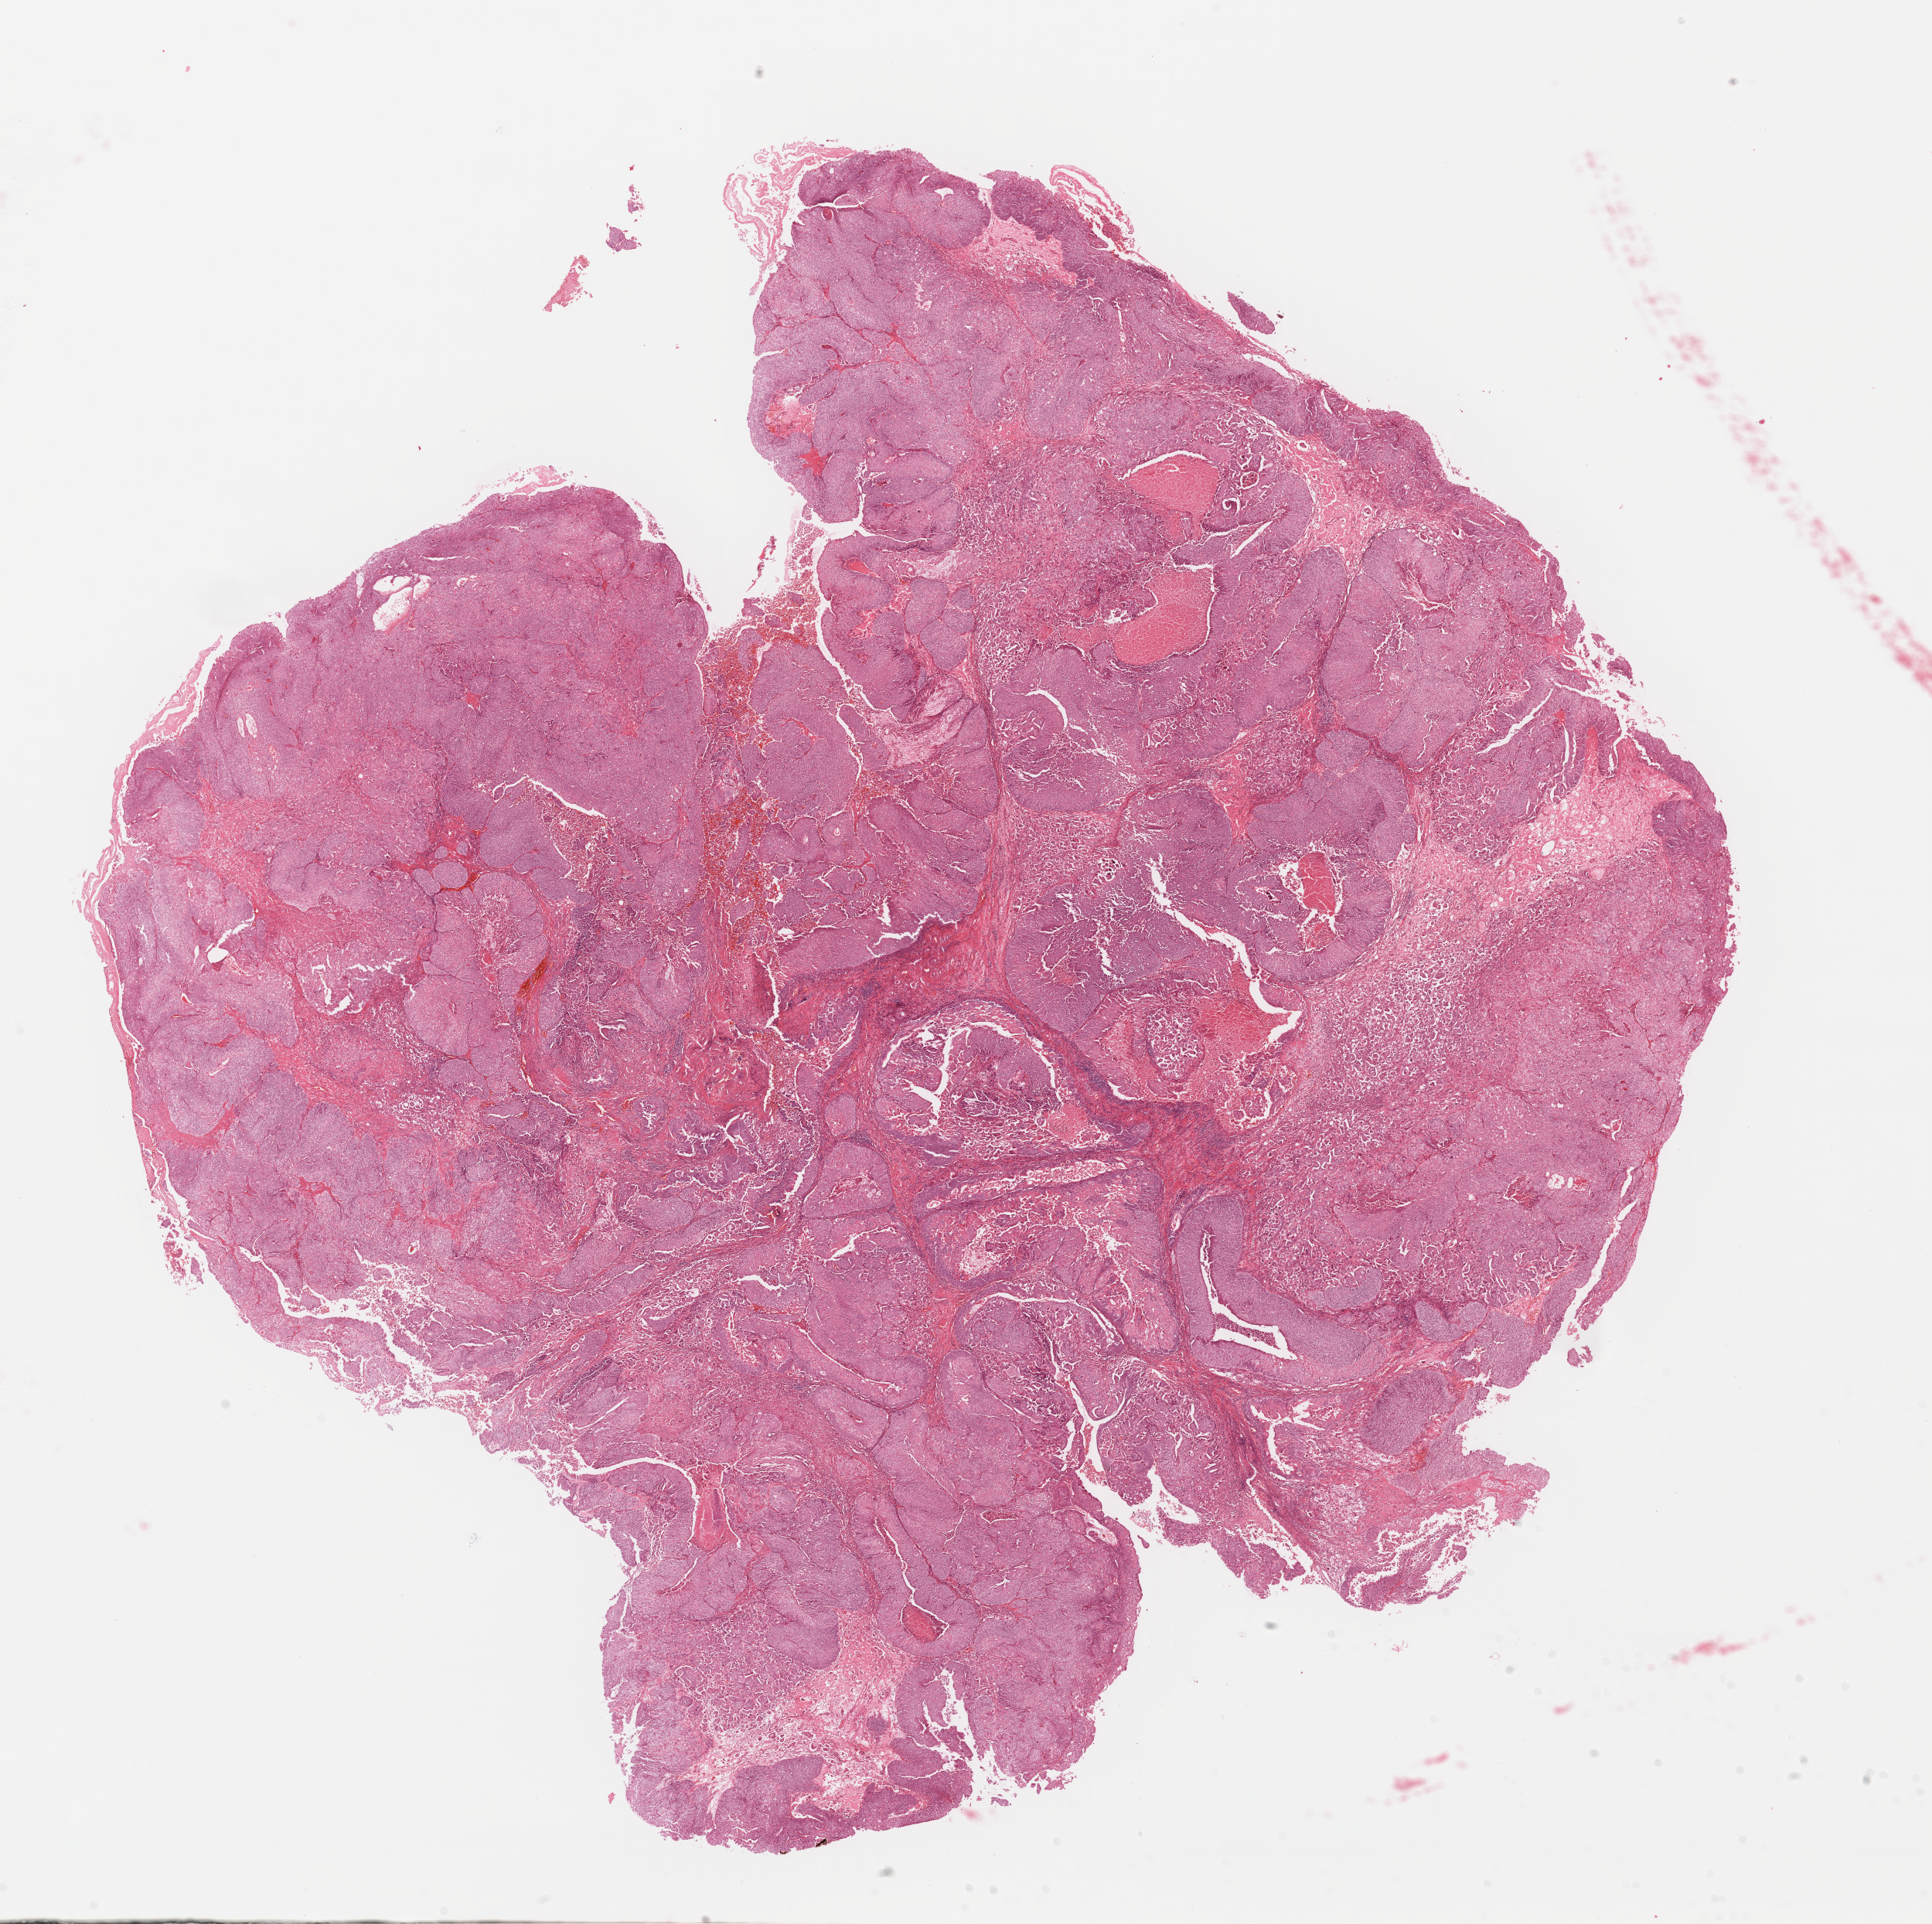
H&E-stained whole-slide image, shown as a low-resolution overview of the whole scanned area (about 19.6 x 19.6 mm, acquisition: 40x scan); FFPE section; bladder, primary tumour sample. Patient: male, age at initial diagnosis 66 years. Histologic grade: high grade.
* histologic diagnosis: Transitional cell carcinoma
* TNM: T2 N0 M0
* AJCC pathologic stage: II (7th edition)